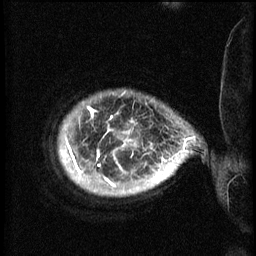
Breast MRI (dynamic contrast-enhanced), one sagittal slice. Slice 55 of 60 in the series (ordered by position). 3 images stored at this slice position (order not interpretable as contrast timing). 1.5 T. TE 4.2 ms, TR 8.2 ms. 2.3 mm slice thickness. 256 × 256 image matrix, field of view 200 × 200 mm. Patient: female, 50 years.
Structures marked on this image (semi-automatically segmented with operator editing):
- analysis volume of interest (the breast-tissue region the enhancement analysis was run in; not a lesion): bounding box <62,96,169,195> (left, top, right, bottom; pixels)
- tumour enhancement mask (voxels above the 70 % enhancement threshold inside the analysis volume of interest): <62,108,169,187>